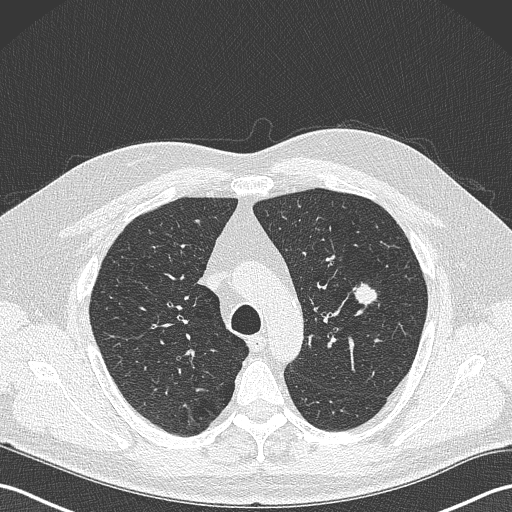
Low-dose screening chest CT, one axial slice. Position 250 of 343 along the scan axis. Reconstruction kernel B50f. Lung window (W 1500 / L -600 HU). 1 mm slice thickness. 512 × 512 image matrix.
Outlined on this slice (manually delineated by an expert):
- lesion 1 (tumor, upper lobe of left lung): bounding box (x1, y1, x2, y2) in pixels: (353, 282, 377, 306)